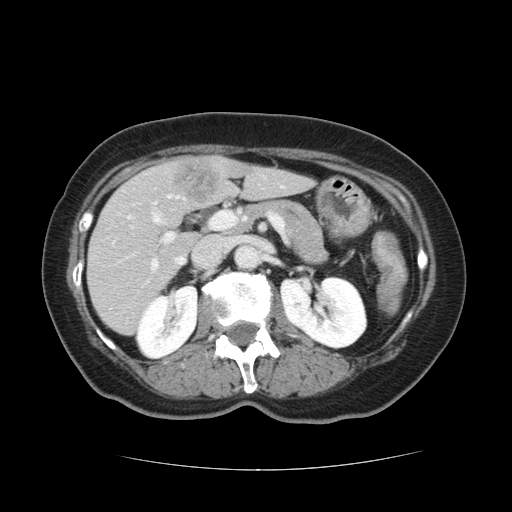
Contrast-enhanced abdominal CT, one axial slice; 120 kVp; intravenous contrast given; soft-tissue window (W 400 / L 40 HU); 512 × 512 image matrix. Female patient, age 67 years. Case-level facts recorded for this patient, not image findings: diagnosis: colorectal cancer liver metastases, imaged before liver resection; multiple liver metastases: yes; largest metastasis: 3 cm; disease in both lobes: yes.
Structures marked on this image (outlined manually by an expert reader):
- hepatic veins: box from (x=129, y=195) to (x=185, y=265) px
- liver: (x=88, y=157)–(x=311, y=335)
- planned liver remnant (the part of the liver to remain after resection): (x=88, y=166)–(x=312, y=335)
- portal vein (with intrahepatic branches): (x=112, y=202)–(x=233, y=271)
- liver metastasis: (x=175, y=164)–(x=219, y=203)